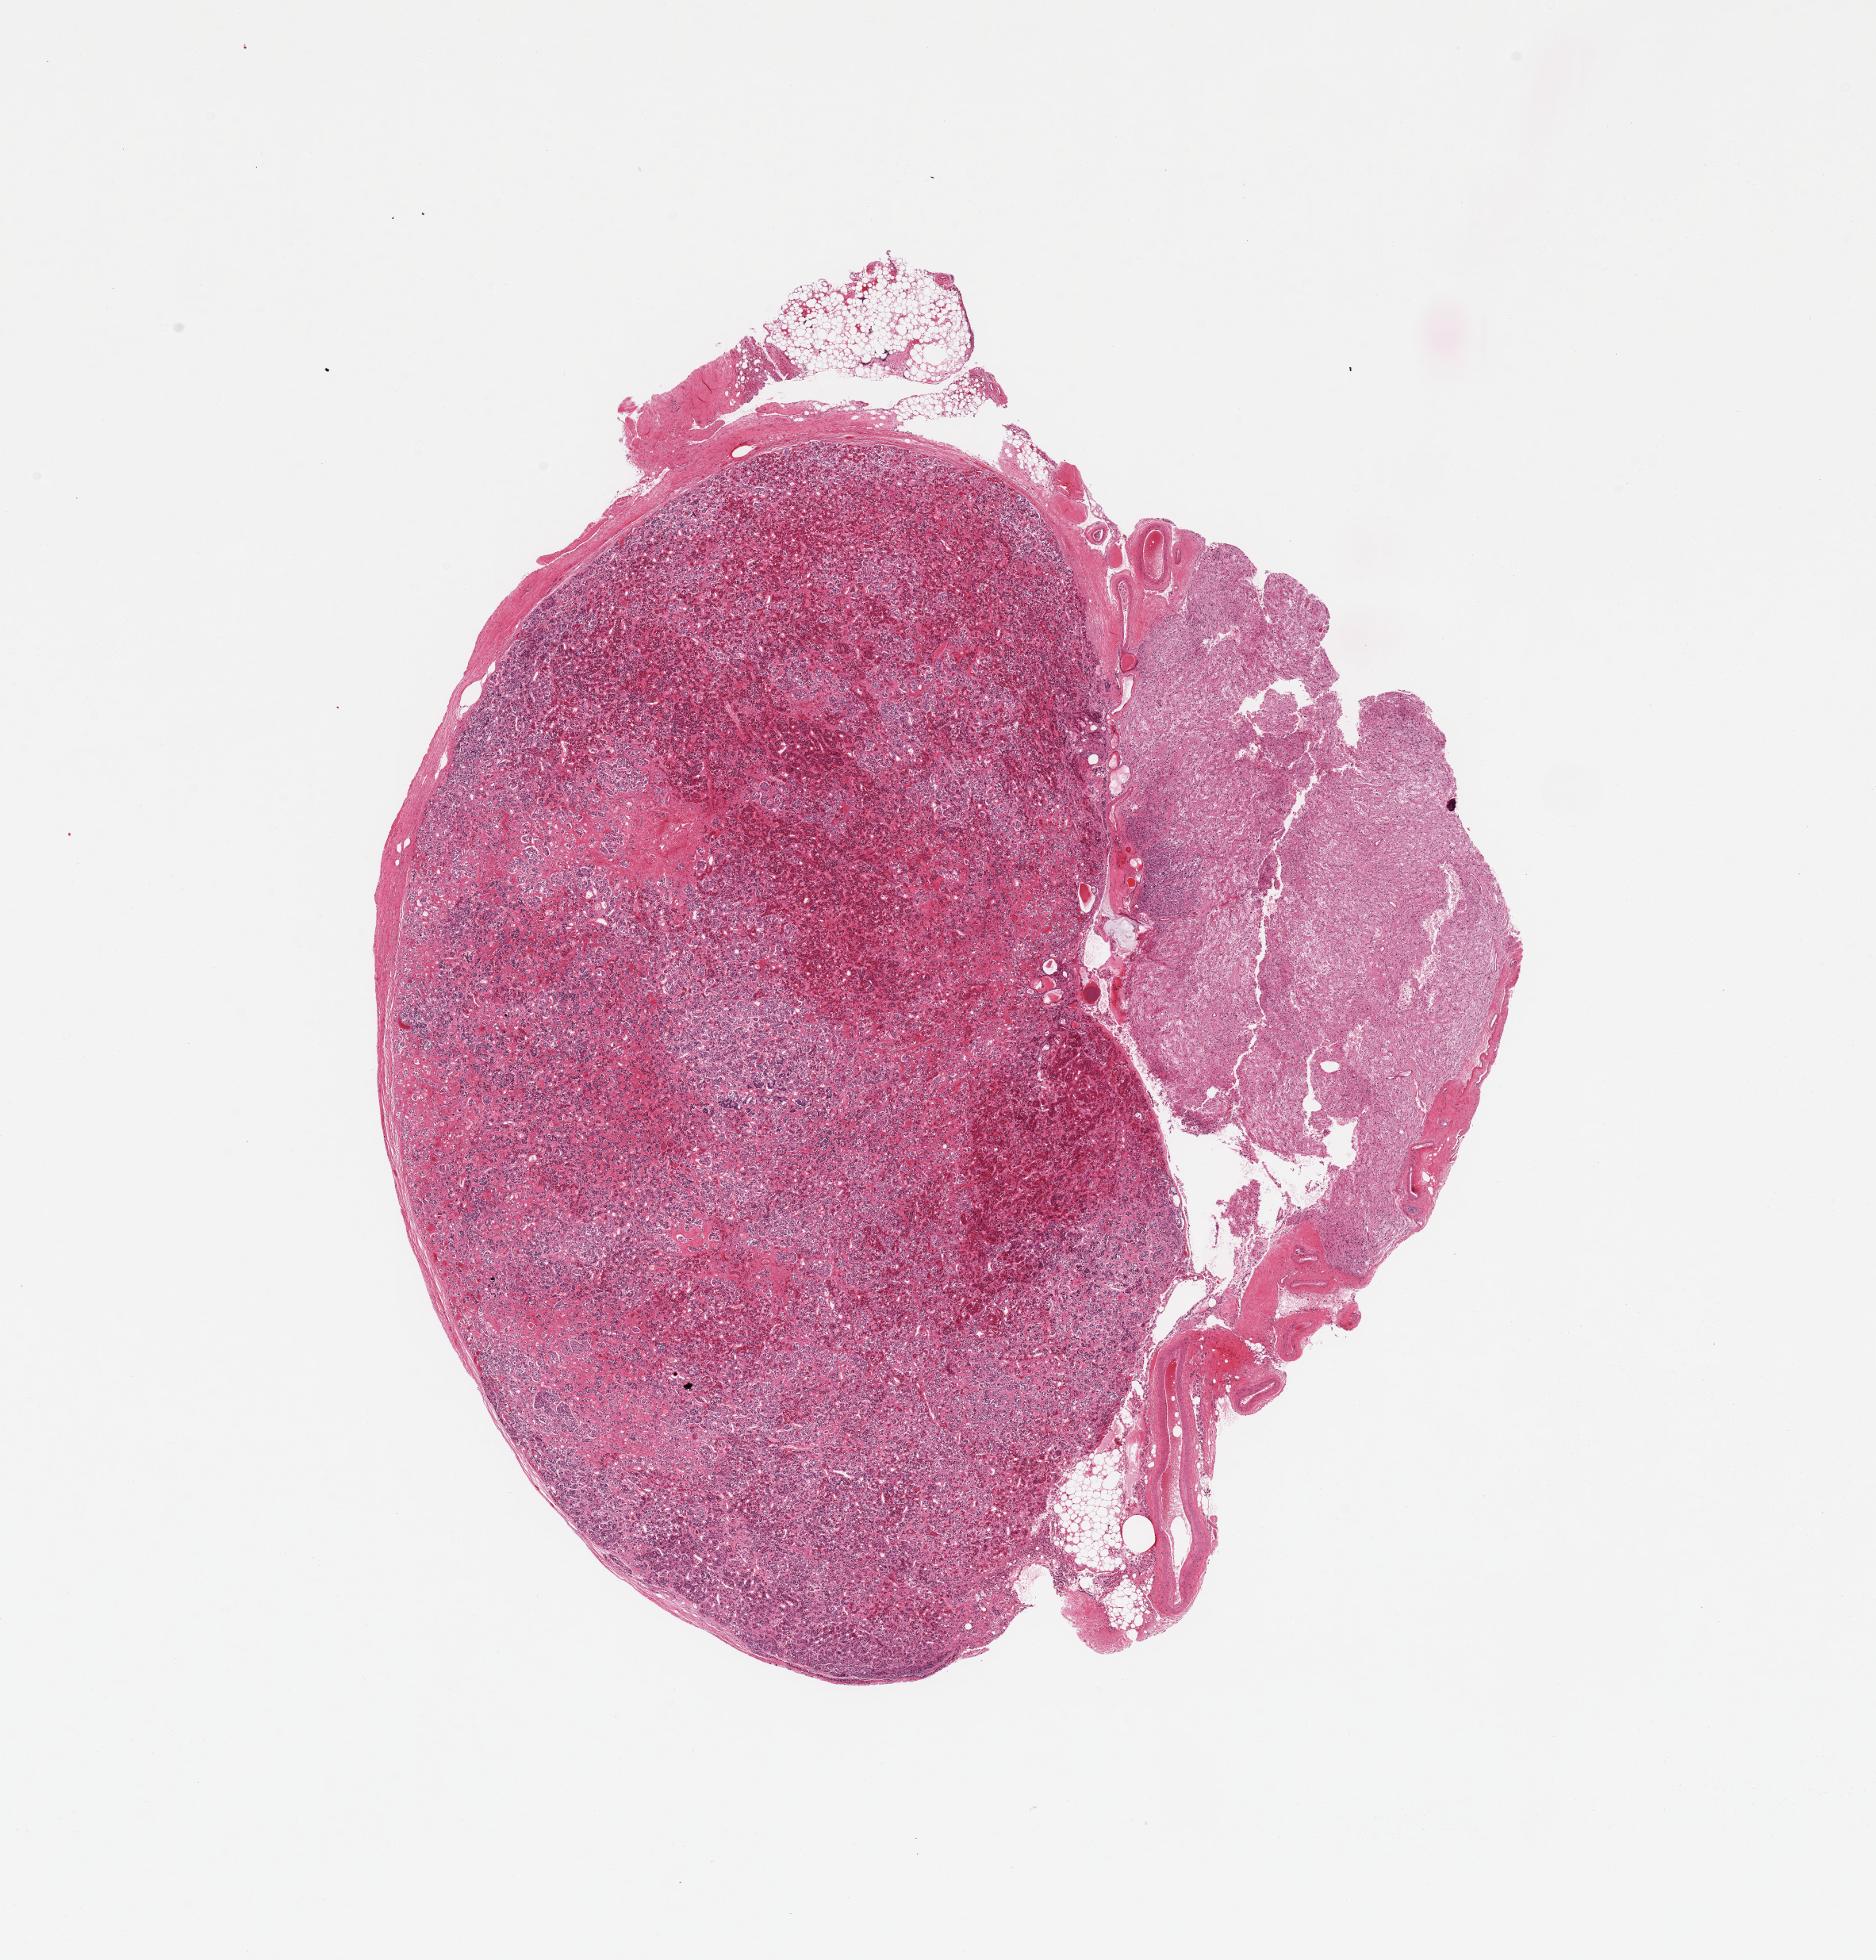
Hematoxylin and eosin (H&E) whole-slide image, brightfield — a low-resolution overview of the entire scanned area, about 18.7 x 19.5 mm (acquisition: 20x scan), PAXgene-fixed paraffin-embedded (PFPE) section, target tissue: pituitary, tissue donor sample. Male donor.
Review note (as recorded): 1 piece; 70% adenohypophysis and 30% neurohypophysis.